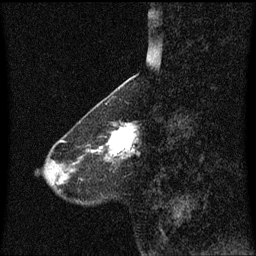
Breast MRI (dynamic contrast-enhanced), one sagittal slice; position 21 of 60 along the scan axis; dynamic contrast-enhanced series, image 2 of 3 at this slice position (ordered by acquisition); 1.5 T; TE 4.2 ms, TR 8.4 ms; 256 × 256 image matrix, field of view 200 × 200 mm. Patient: female, 58 years.
Outlined on this slice (semi-automatically segmented with operator editing):
- analysis volume of interest (the breast-tissue region the enhancement analysis was run in; not a lesion): box from (x=100, y=121) to (x=139, y=160) px
- tumour enhancement mask (voxels above the 70 % enhancement threshold inside the analysis volume of interest): (x=100, y=124)–(x=137, y=156)